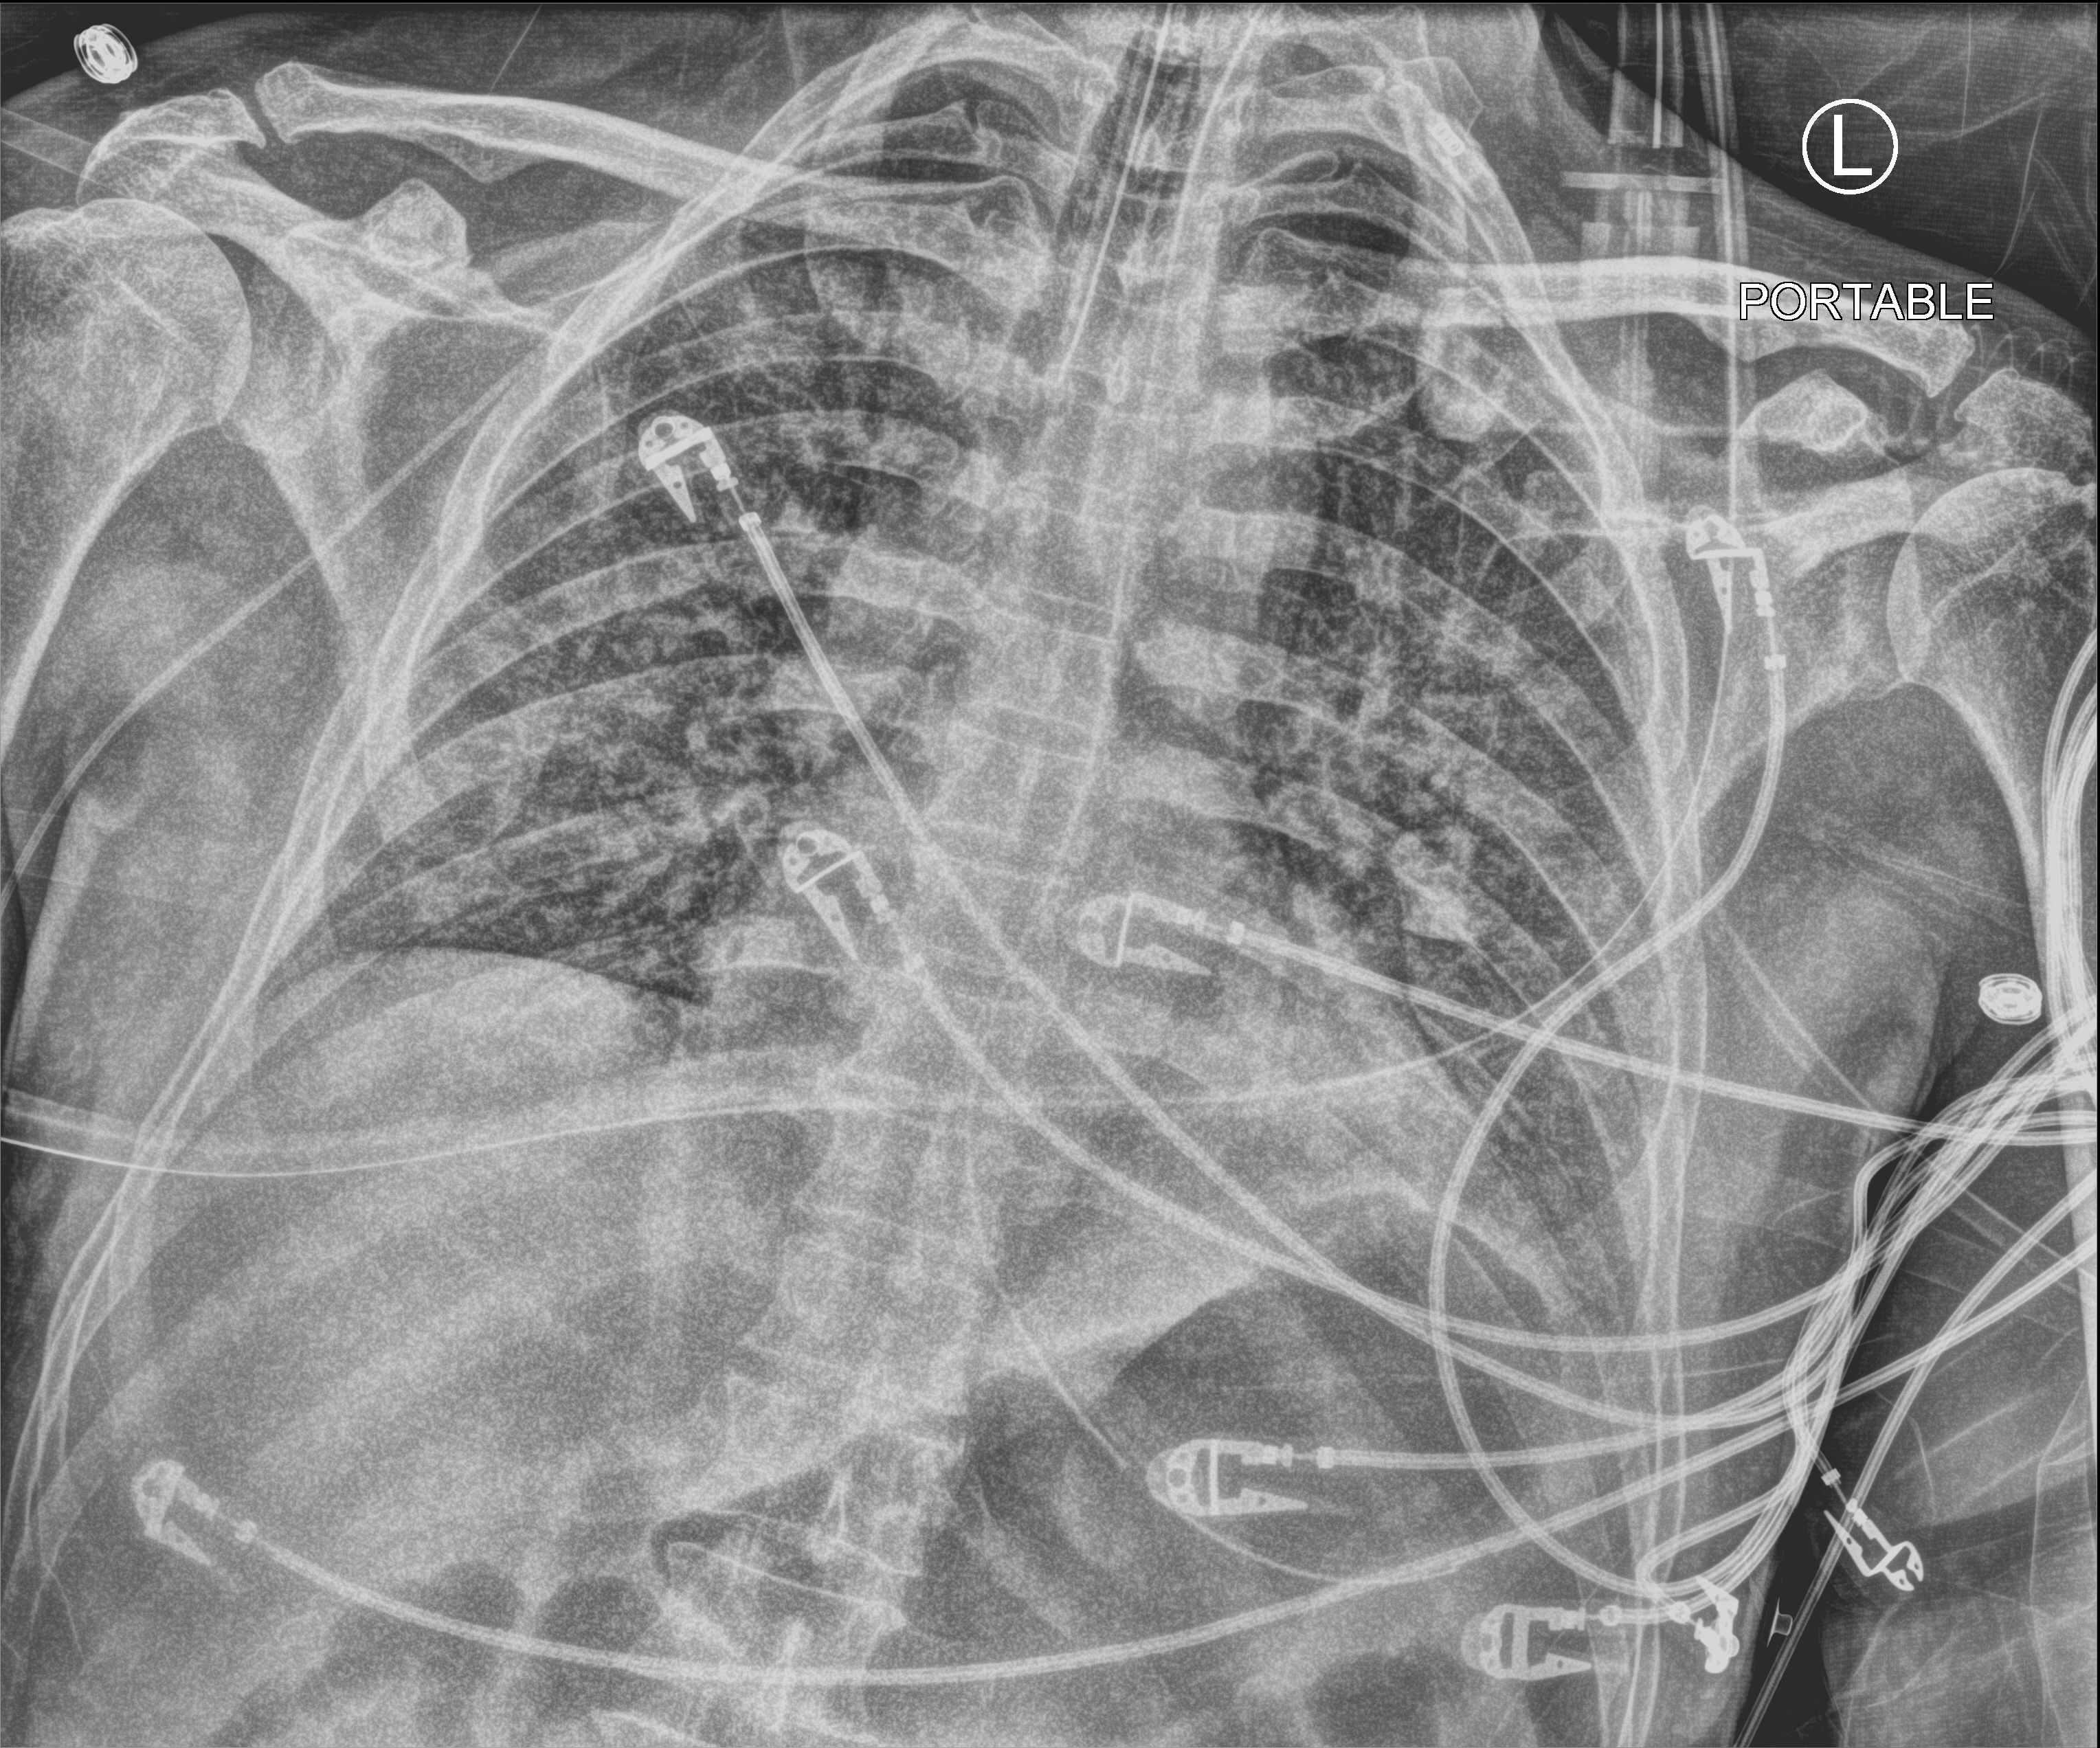
Chest X-ray (portable), anteroposterior (AP) projection. Male patient hospitalised with COVID-19, age 60–74 years.
Hospital-stay facts (about this admission, not read from this image; timing relative to this image not recorded):
- diabetes (admission record): yes